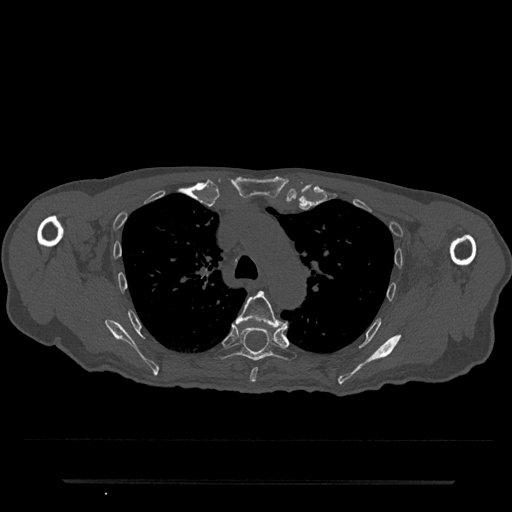
CT including the spine, one axial slice; slice 550 of 797 in the series (ordered by position); reconstruction kernel Br40s/3; bone window (W 1800 / L 400 HU); 0.5 mm slice thickness; 512 × 512 image matrix, field of view 427 × 427 mm. Male patient, age 74 years. Case-level facts recorded for this patient, not image findings: primary cancer: prostate.
Structures marked on this image (semi-automatically segmented with operator editing):
- T5 vertebra: box from (x=236, y=291) to (x=288, y=383) px
- T6 vertebra: (x=215, y=322)–(x=297, y=361)